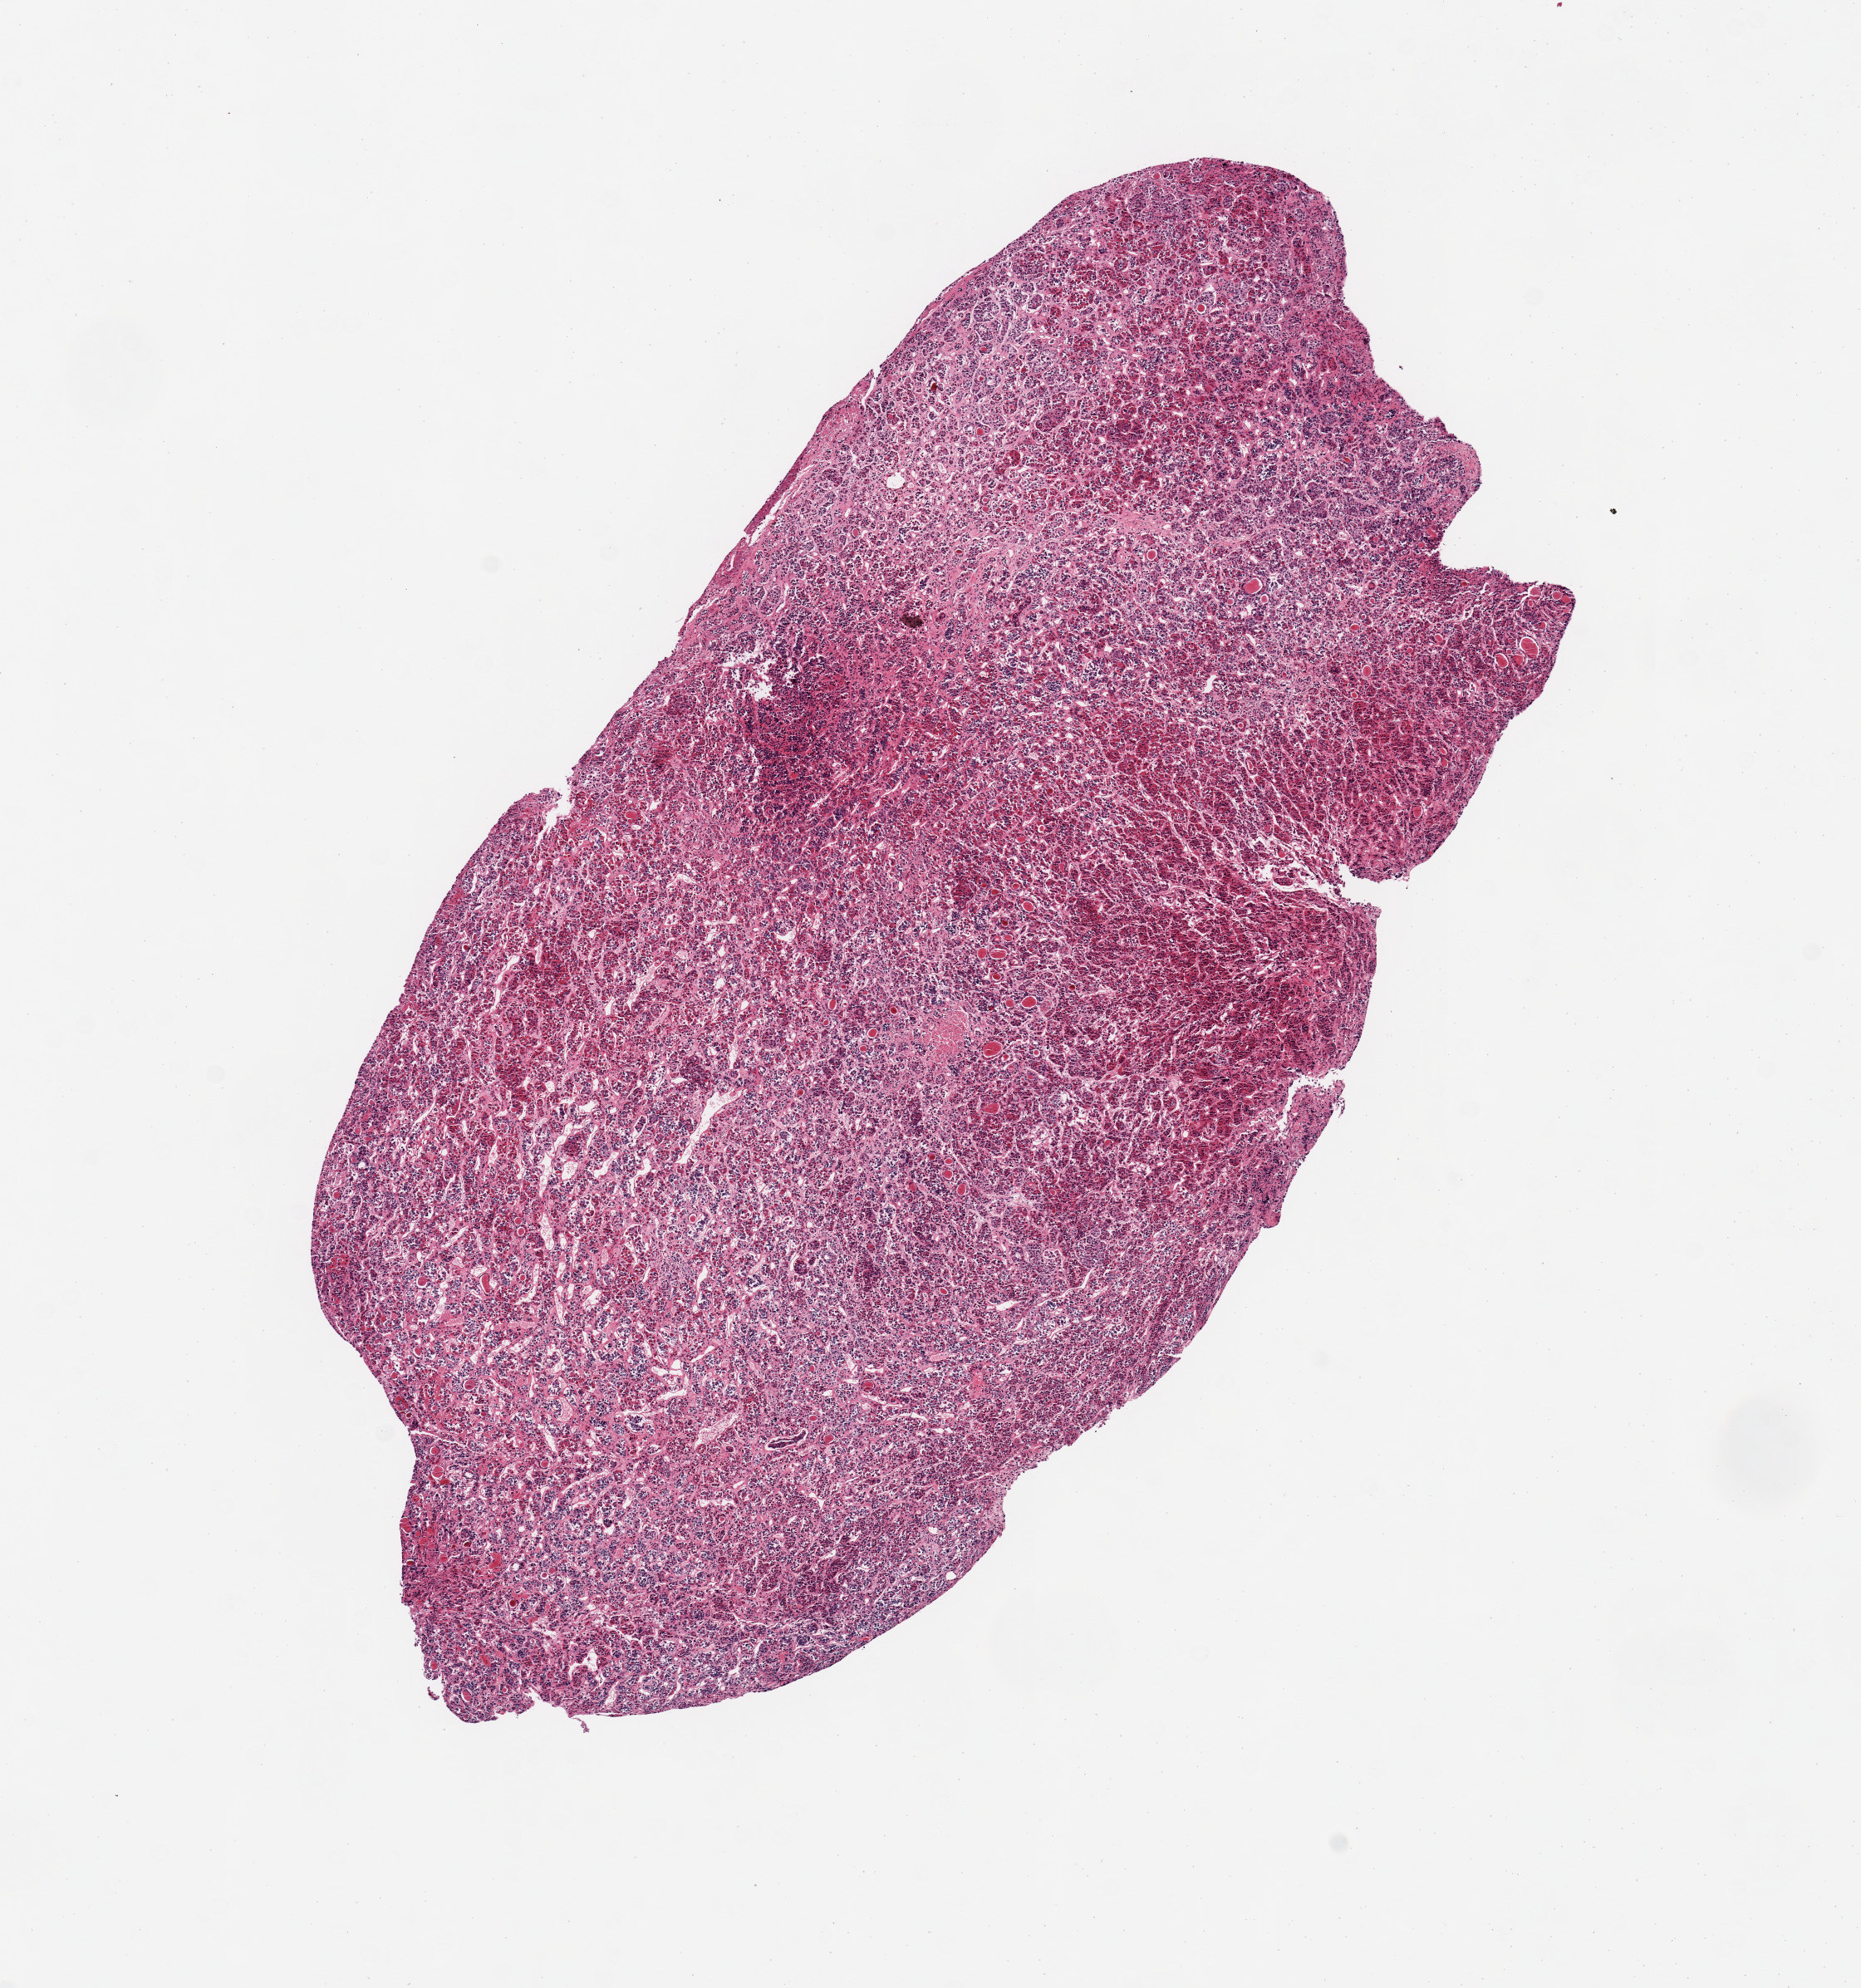
Digitized hematoxylin and eosin (H&E)-stained section — low-resolution overview of the scanned area, about 8.9 x 9.5 mm, PAXgene-fixed paraffin-embedded (PFPE) section, section of pituitary (target tissue), tissue donor sample.
Pathologist's review note for this sample: 1 piec, adenohypophysis only.